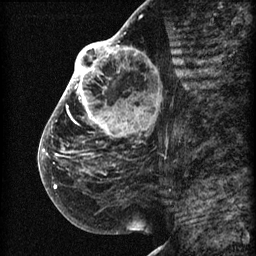
Breast MRI (dynamic contrast-enhanced), one sagittal slice; slice 32 of 60 in the series (ordered by position); 3 images stored at this slice position (order not interpretable as contrast timing); 1.5 T; TE 4.2 ms, TR 22.7 ms; 2 mm slice thickness; 256 × 256 image matrix. Female patient, age 48 years. From the clinical record (not read from this slice): setting: breast cancer imaged before/during neoadjuvant chemotherapy; receptor status: triple-negative.
Outlined on this slice (semi-automatic segmentation, software-assisted and operator-edited):
- analysis volume of interest (the breast-tissue region the enhancement analysis was run in; not a lesion): bounding box <44,30,173,207> (left, top, right, bottom; pixels)
- tumour enhancement mask (voxels above the 90 % enhancement threshold inside the analysis volume of interest): <44,31,138,189>